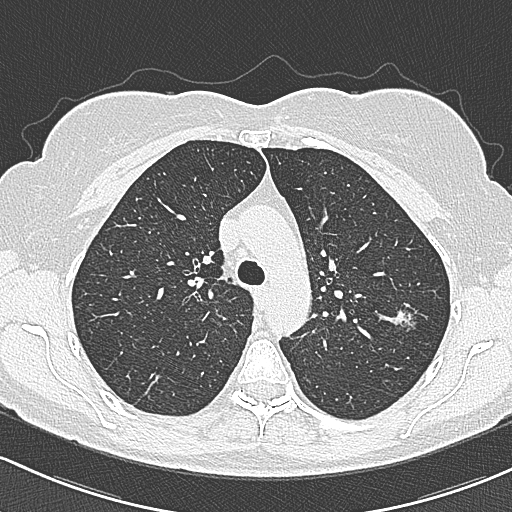
Low-dose screening chest CT, axial slice; first (baseline) screen; lung window (W 1500 / L -600 HU); 1 mm slice thickness; lung (sharp) reconstruction kernel (B80f); slice 90 of 312 in the series. Female participant, aged 65 years at enrolment.
Expert reader's lesion annotation, bounding box [x1, y1, x2, y2] px = [385, 300, 425, 338]. The screening reader recorded 3 non-calcified nodules or masses ≥4 mm on this exam; which of them this box marks is not recorded. Participant outcome: lung cancer diagnosed 390 days after this screen — bronchiolo-alveolar carcinoma, non-mucinous, left upper lobe, stage IA (AJCC 6th edition), 10 mm at pathology.